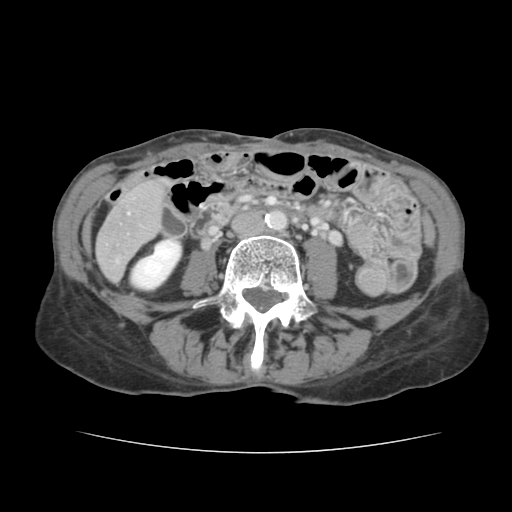
Contrast-enhanced abdominal CT, one axial slice; slice 25 of 136 in the series (ordered by position); intravenous contrast given; soft-tissue window (W 400 / L 40 HU); 2.5 mm slice thickness; 512 × 512 image matrix. Female patient, age 77 years. From the clinical record (not read from this slice): diagnosis: colorectal cancer liver metastases, imaged before liver resection; multiple liver metastases: yes; largest metastasis: 3 cm; disease in both lobes: no.
Structures marked on this image (outlined manually by an expert reader):
- liver: bounding box (x1, y1, x2, y2) in pixels: (98, 182, 164, 279)